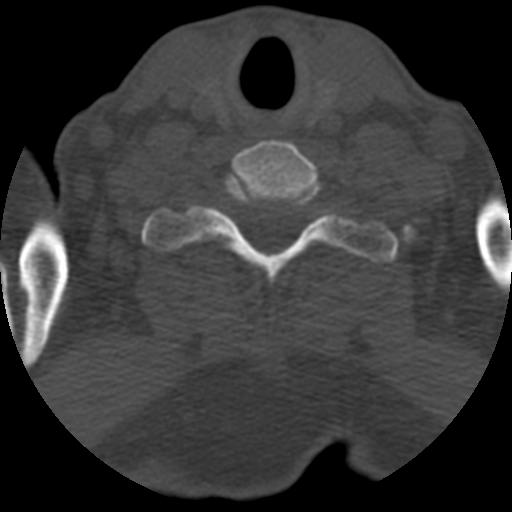
CT including the spine, one axial slice; position 524 of 708 along the scan axis; reconstruction kernel STANDARD; 120 kVp; one of 3 acquisitions stored at this slice position; bone window (W 1800 / L 400 HU); 1.25 mm slice thickness; 512 × 512 image matrix, field of view 160 × 160 mm. Patient age 55 years. From the clinical record (not read from this slice): primary cancer: colon.
Structures marked on this image (semi-automatic segmentation, software-assisted and operator-edited):
- T1 vertebra: bounding box (x1, y1, x2, y2) in pixels: (142, 179, 396, 286)